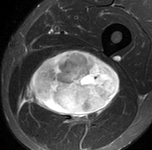
MRI of an extremity soft-tissue mass, one axial slice. Slice 65 of 90 in the series (ordered by position). STIR. MR volume resampled by the dataset authors to the PET/CT grid (not the native acquisition matrix). 3.27 mm slice thickness. 152 × 150 image matrix, field of view 148 × 146 mm. Male patient. From the clinical record (not read from this slice): histological type: undifferentiated pleomorphic liposarcoma; grade: high; site of the primary tumour: left thigh.
Annotated regions visible in this slice (expert contour drawn on MRI and transferred to this co-registered scan by the dataset authors):
- gross tumour volume including surrounding oedema: bounding box <20,50,119,127> (left, top, right, bottom; pixels)
- gross tumour volume (mass): <25,50,119,118>